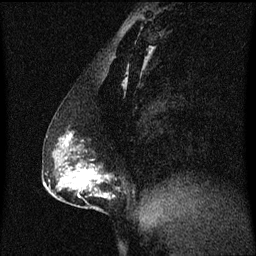
Breast MRI (dynamic contrast-enhanced), one sagittal slice; slice 31 of 60 in the series (ordered by position); dynamic contrast-enhanced series, image 2 of 3 at this slice position (ordered by acquisition); 1.5 T; TE 4.2 ms, TR 8.4 ms; 2 mm slice thickness; 256 × 256 image matrix, field of view 200 × 200 mm. Patient: female, 40 years. Case-level facts recorded for this patient, not image findings: setting: breast cancer imaged before/during neoadjuvant chemotherapy; receptor status: triple-negative.
Outlined on this slice (semi-automatically segmented with operator editing):
- analysis volume of interest (the breast-tissue region the enhancement analysis was run in; not a lesion): bounding box <58,132,119,211> (left, top, right, bottom; pixels)
- tumour enhancement mask (voxels above the 70 % enhancement threshold inside the analysis volume of interest): <66,136,109,199>